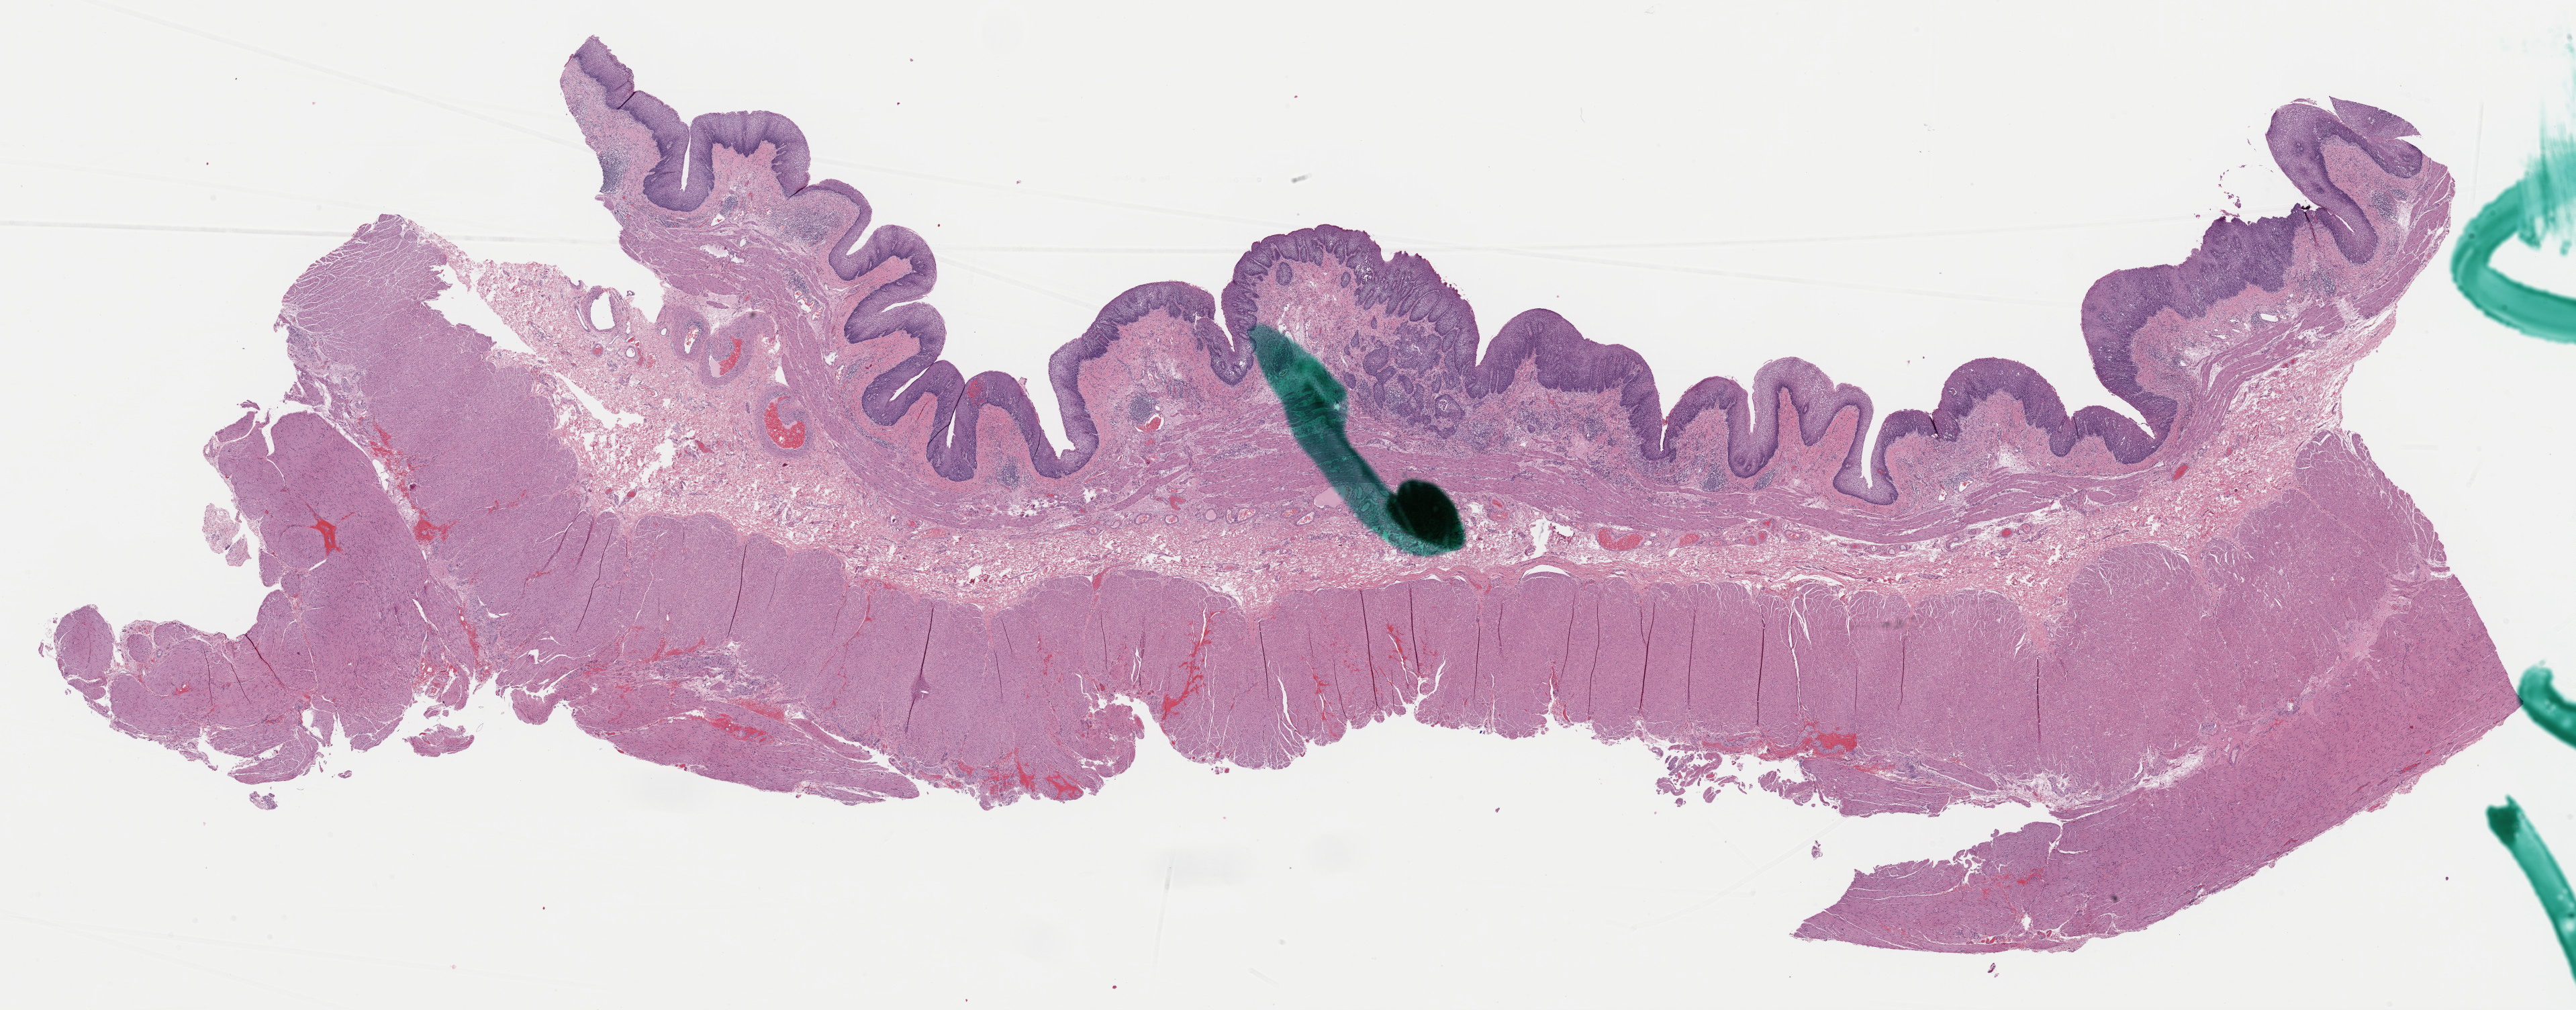
Hematoxylin and eosin (H&E) stained whole-slide image, low-resolution overview of the scanned area, about 30.3 x 11.9 mm; formalin-fixed paraffin-embedded (FFPE) diagnostic section; sample: primary tumour, esophagus. Female patient; age at initial diagnosis 54 years. Histologic grade: GX (grade cannot be assessed).
Pathologic diagnosis: Basaloid squamous cell carcinoma. TNM: T1 N0. AJCC pathologic stage: IA (7th edition). Lymph nodes positive (case pathology): 0 of 3 examined.